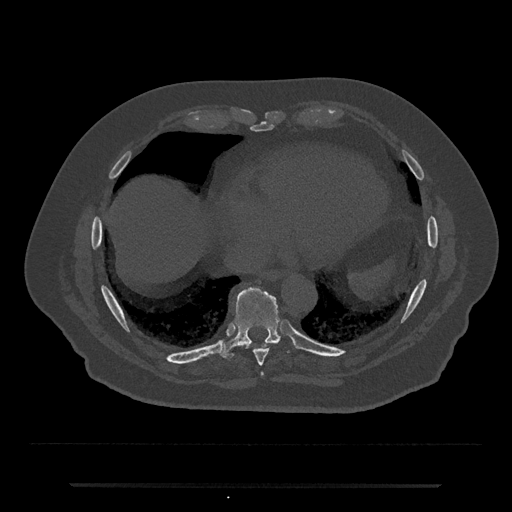
CT including the spine, one axial slice; slice 777 of 797 in the series (ordered by position); reconstruction kernel Br40s/3; 120 kVp; bone window (W 1800 / L 400 HU); 0.5 mm slice thickness; 512 × 512 image matrix, field of view 434 × 434 mm. Patient: male, 80 years. Case-level facts recorded for this patient, not image findings: primary cancer: prostate.
Annotated regions visible in this slice (semi-automatically segmented with operator editing):
- T8 vertebra: box from (x=254, y=343) to (x=278, y=366) px
- T9 vertebra: (x=218, y=287)–(x=296, y=360)